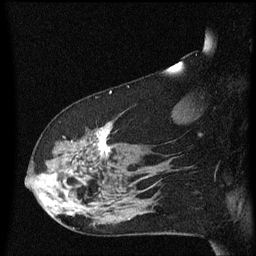
Breast MRI (dynamic contrast-enhanced), one sagittal slice. Slice 41 of 60 in the series (ordered by position). Dynamic contrast-enhanced series, image 2 of 3 at this slice position (ordered by acquisition). 1.5 T. TE 4.2 ms, TR 8.4 ms. 2 mm slice thickness. 256 × 256 image matrix, field of view 200 × 200 mm. Patient: female, 48 years.
Outlined on this slice (semi-automatically segmented with operator editing):
- analysis volume of interest (the breast-tissue region the enhancement analysis was run in; not a lesion): box from (x=31, y=122) to (x=134, y=225) px
- tumour enhancement mask (voxels above the 70 % enhancement threshold inside the analysis volume of interest): (x=41, y=126)–(x=110, y=211)